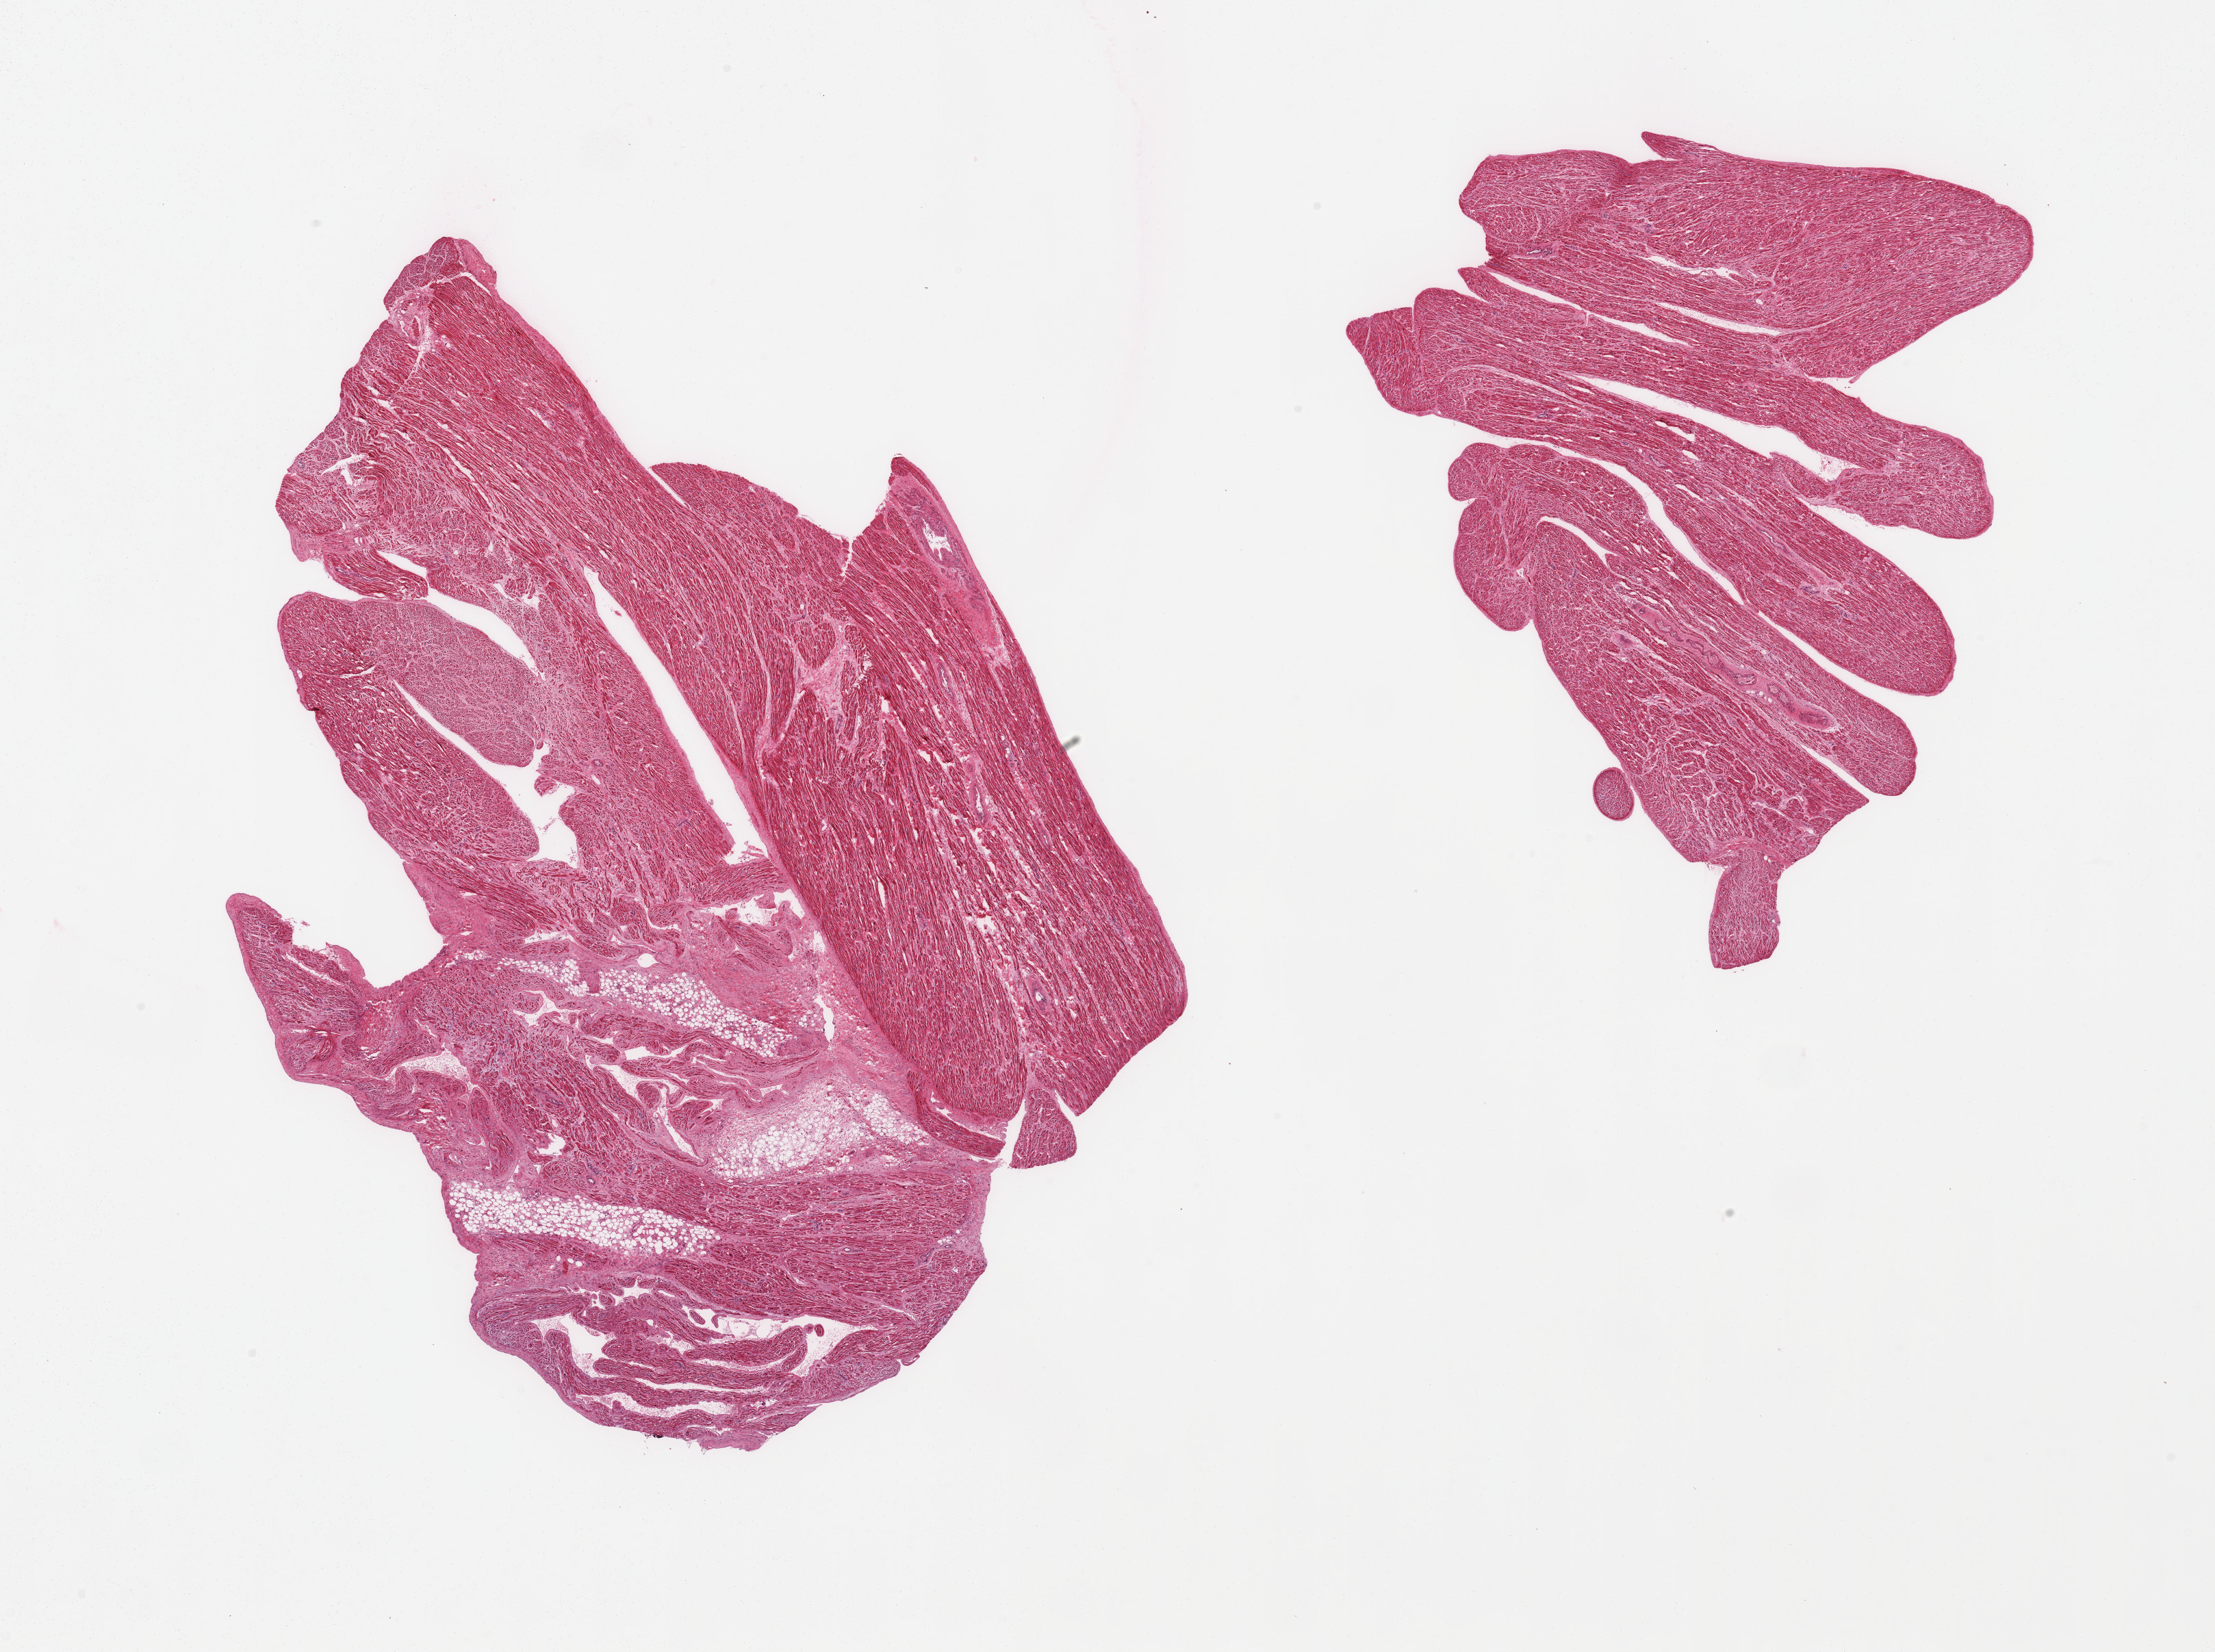
Hematoxylin and eosin (H&E) whole-slide image — shown as a low-resolution overview of the whole scanned area (about 25.6 x 19.1 mm). PAXgene-fixed, paraffin-embedded tissue. Section of auricular appendage (target tissue). Tissue donor sample.
• reviewer comment on this tissue sample: 2 pieces, no abnormalities